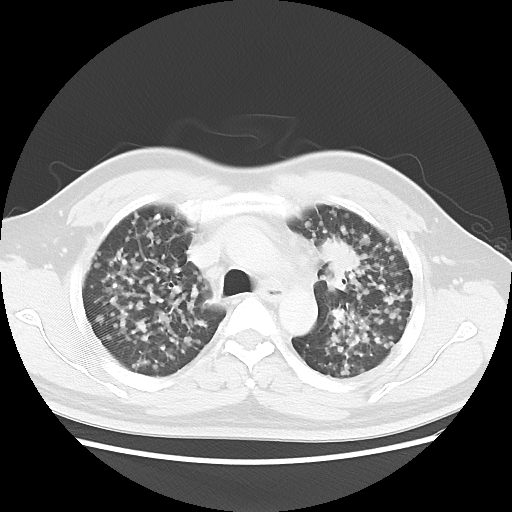
Chest CT, one axial slice. Position 28 of 40 along the scan axis. Reconstruction kernel LUNG. 120 kVp. Lung window (W 1500 / L -600 HU). 512 × 512 image matrix. Patient: male, 41 years. Case-level facts recorded for this patient, not image findings: clinical TNM (as recorded): T1c N3 M1b.
Structures marked on this image (rectangle marked by the reading radiologist):
- lung tumour (recorded histology: adenocarcinoma): box from (x=315, y=233) to (x=372, y=284) px